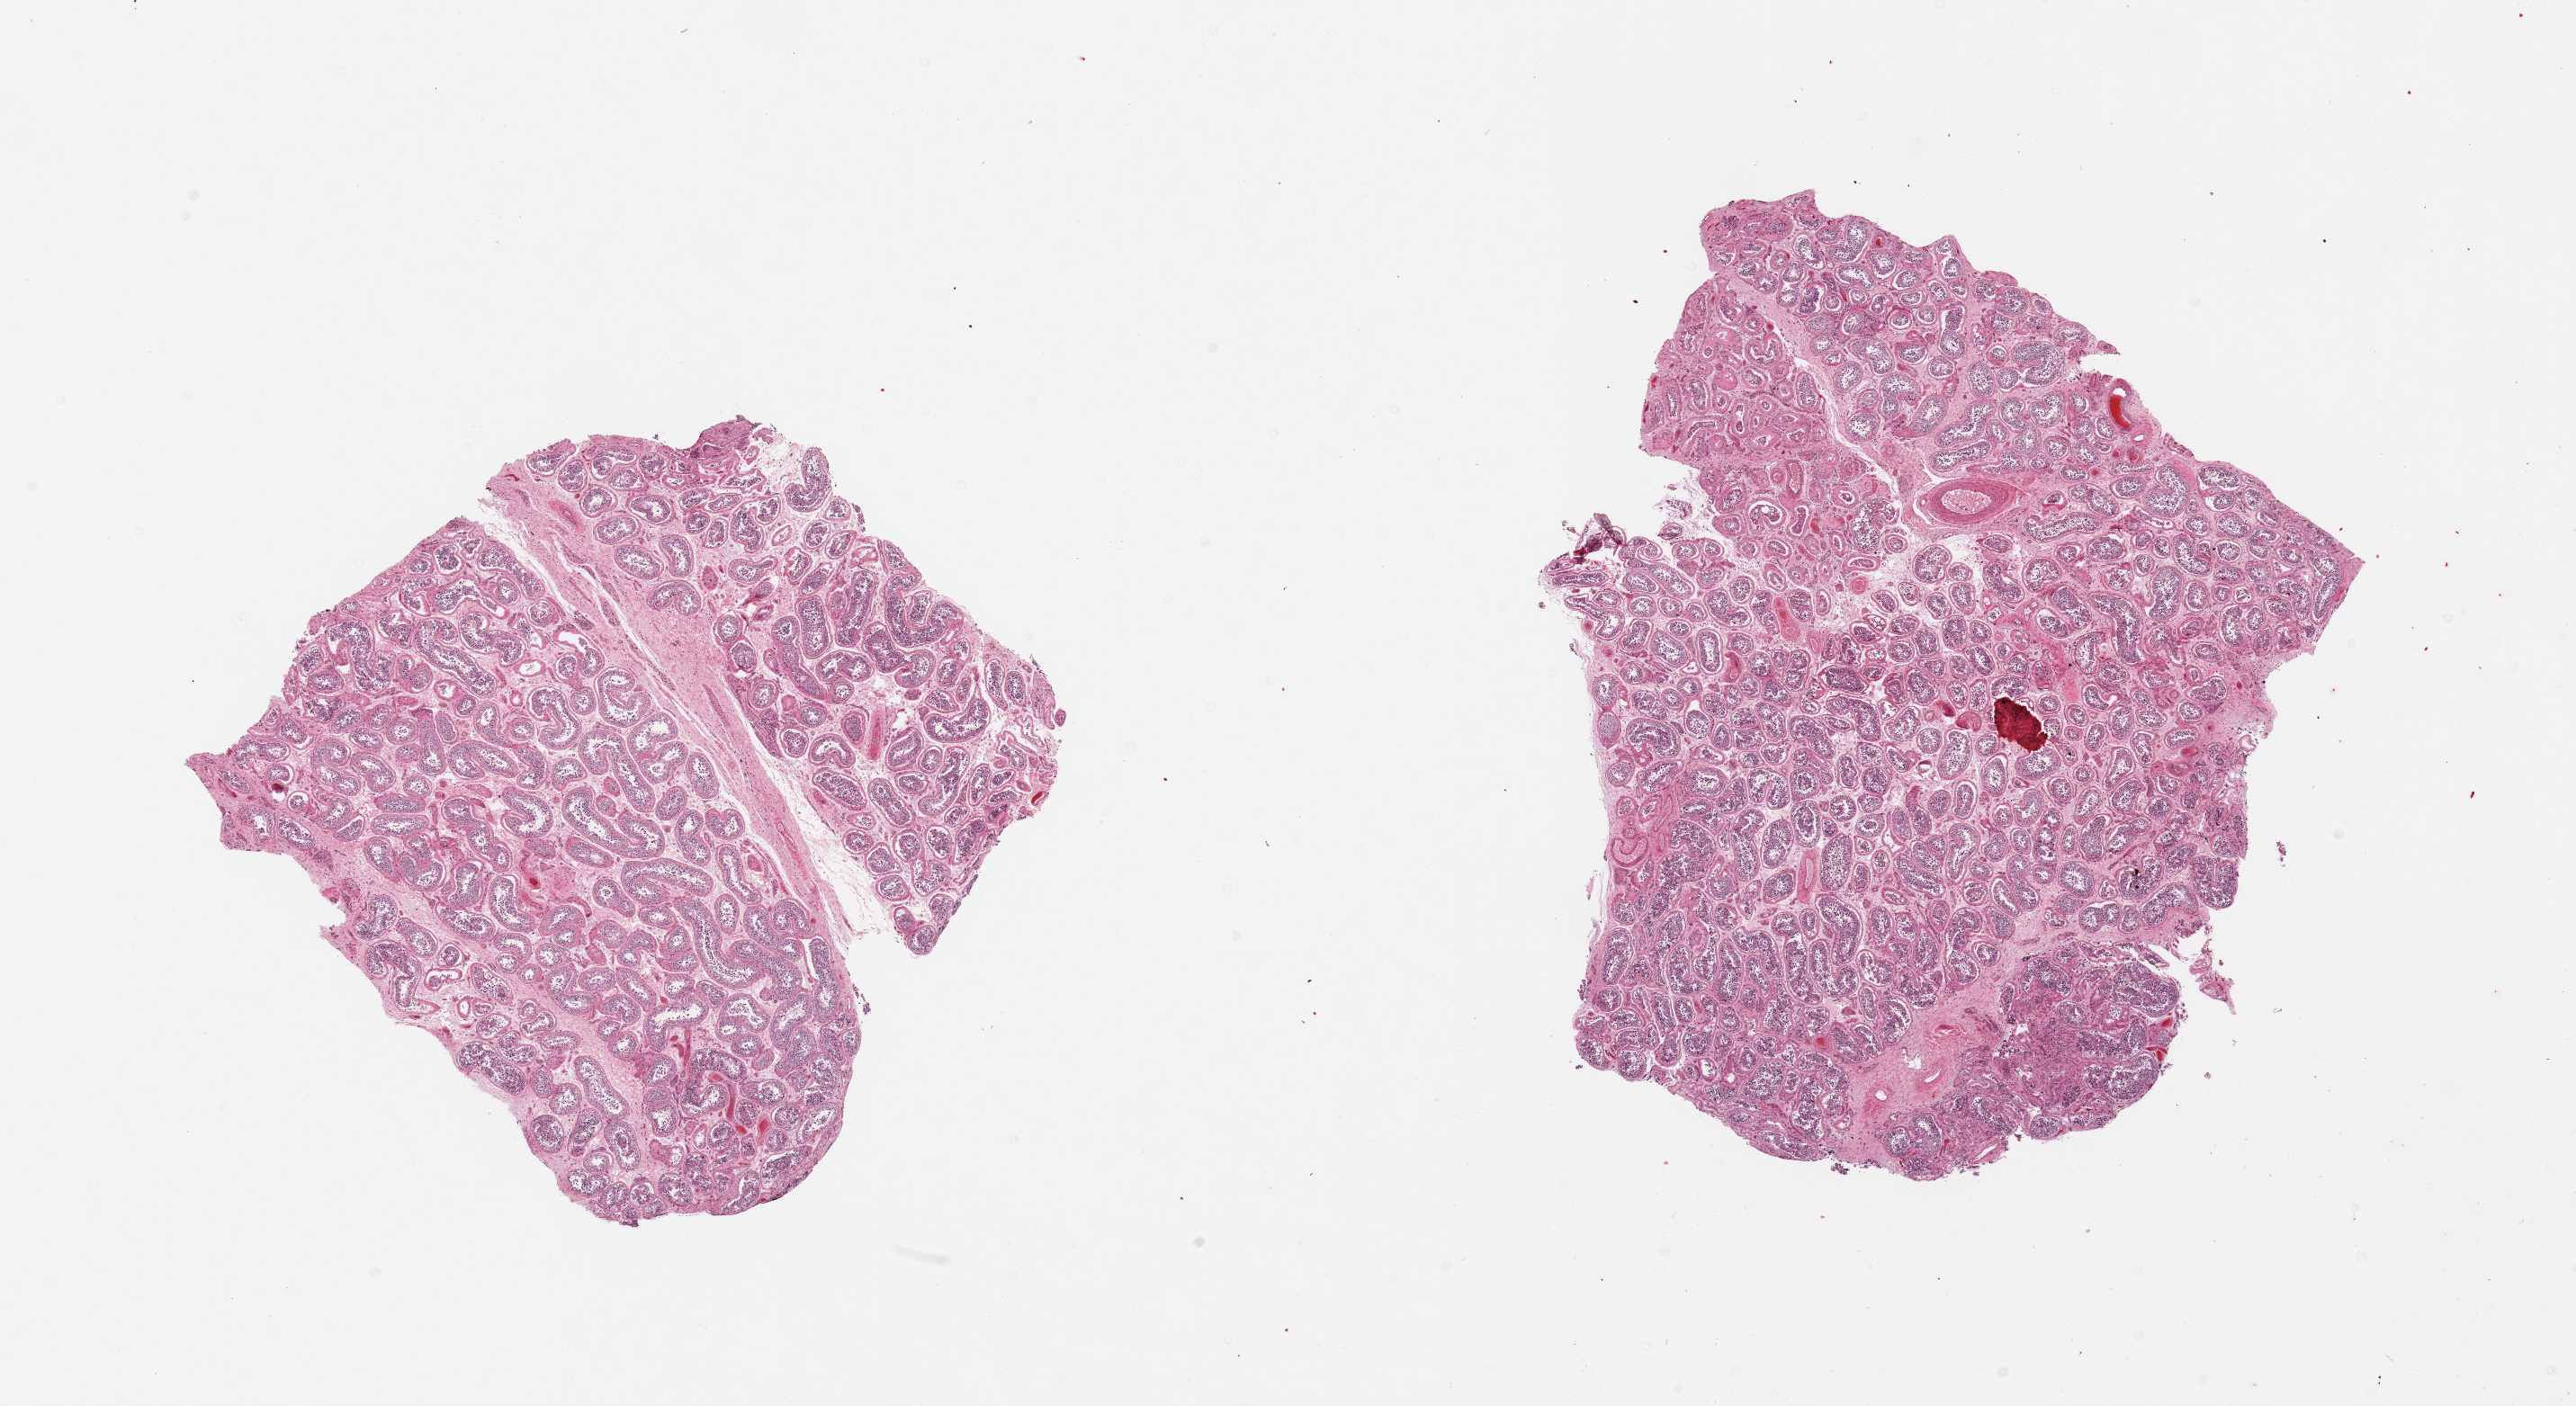
Whole-slide image, H&E stain — low-resolution overview of the scanned area, about 22.6 x 12.4 mm (acquisition: 20x scan), PAXgene-fixed paraffin-embedded (PFPE) section, section of testis (target tissue), donor tissue sample.
- pathologist's review note for this sample: 2 pieces; some hyalinization of tubules, reduced/absent spermatogenesis